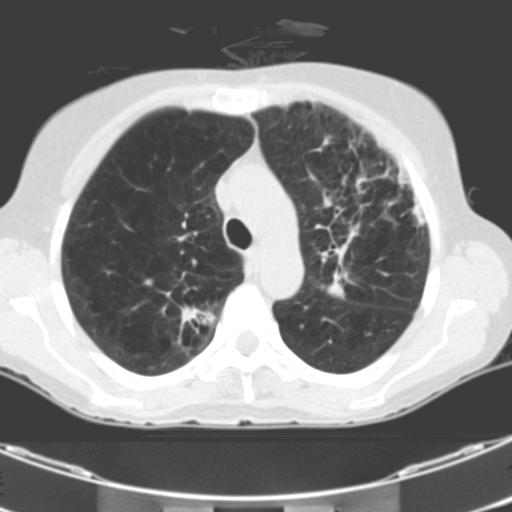
Low-dose screening chest CT, one axial slice; slice 78 of 106 in the series (ordered by position); one of 2 acquisitions stored at this slice position; lung window (W 1500 / L -600 HU); 512 × 512 image matrix, field of view 299 × 299 mm.
Annotated regions visible in this slice (manually delineated by an expert):
- lesion 1 (tumor): bounding box (x1, y1, x2, y2) in pixels: (327, 282, 344, 299)